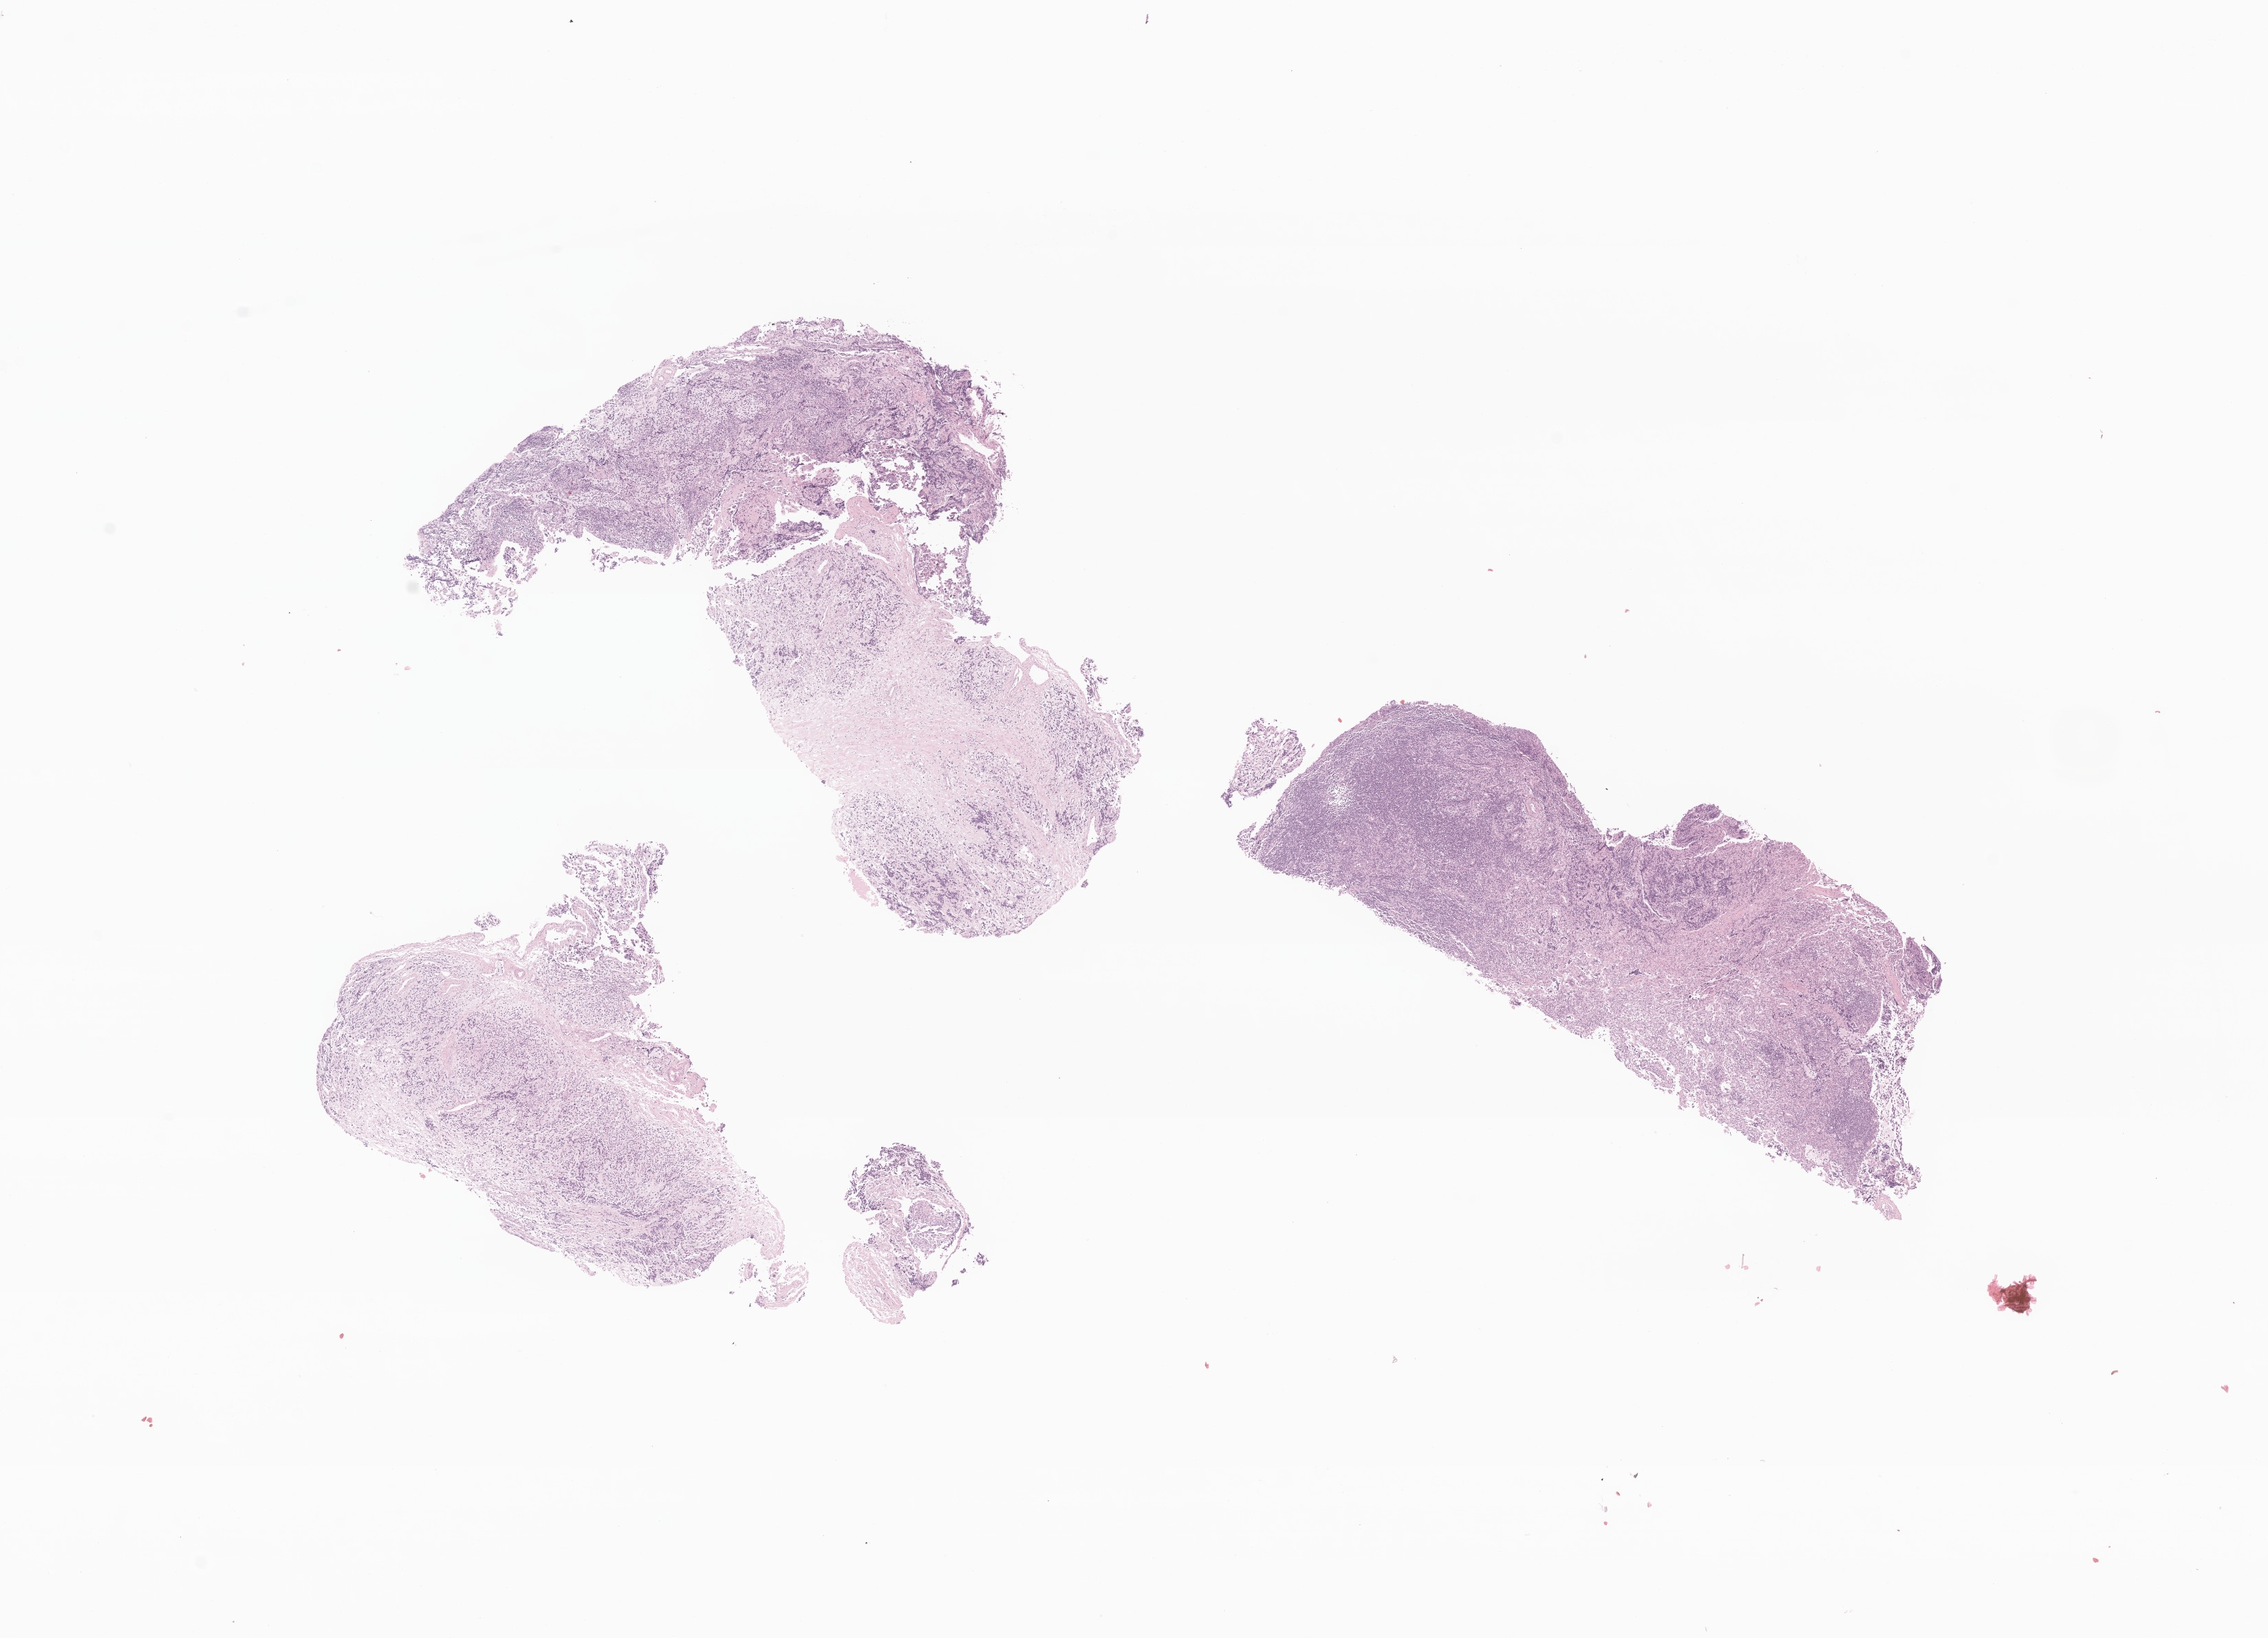
Digitized haematoxylin and eosin-stained section of tumor tissue from the soft tissue of thorax, low-resolution overview of the scanned area, about 13.9 x 10.0 mm, formalin-fixed paraffin-embedded section. Patient: female, age 189 days.
Diagnosis (ICD-O-3 morphology term): Neuroblastoma, NOS.